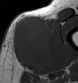
MRI of an extremity soft-tissue mass, one axial slice; slice 17 of 43 in the series (ordered by position); MR volume resampled by the dataset authors to the PET/CT grid (not the native acquisition matrix); 78 × 83 image matrix. Male patient. Case-level facts recorded for this patient, not image findings: histological type: pleiomorphic leiomyosarcoma; grade: high; site of the primary tumour: left thigh.
Structures marked on this image (expert contour drawn on MRI and transferred to this co-registered scan by the dataset authors):
- gross tumour volume including surrounding oedema: bounding box <11,15,60,68> (left, top, right, bottom; pixels)
- gross tumour volume (mass): <11,17,55,68>